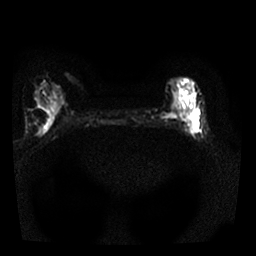
Breast MRI, one axial slice; diffusion-weighted series; image 2 of 4 stored at this slice position (different b-values; order by instance number); 1.5 T; 4 mm slice thickness; 256 × 256 image matrix. Female patient.
Structures marked on this image (expert manual segmentation):
- tumour on diffusion-weighted imaging: bounding box <191,109,198,136> (left, top, right, bottom; pixels)